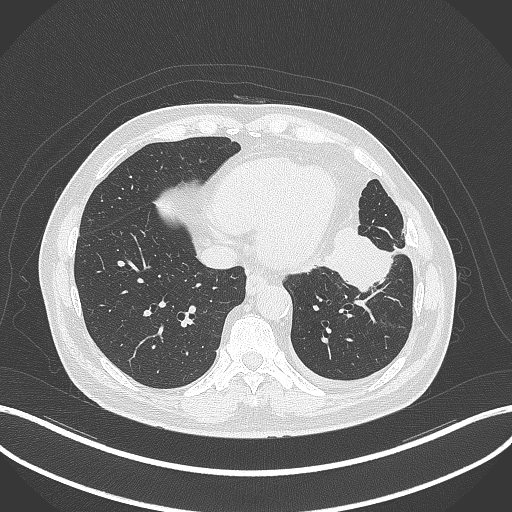
Chest CT, one axial slice. Reconstruction kernel B70f. 120 kVp. Lung window (W 1500 / L -600 HU). 1 mm slice thickness. 512 × 512 image matrix, field of view 400 × 400 mm. Patient: male, 68 years. Case-level facts recorded for this patient, not image findings: clinical TNM (as recorded): T2b N0 M0.
Annotated regions visible in this slice (bounding box drawn by a radiologist):
- lung tumour (recorded histology: squamous cell carcinoma): bounding box [x1, y1, x2, y2] px = [321, 225, 396, 293]